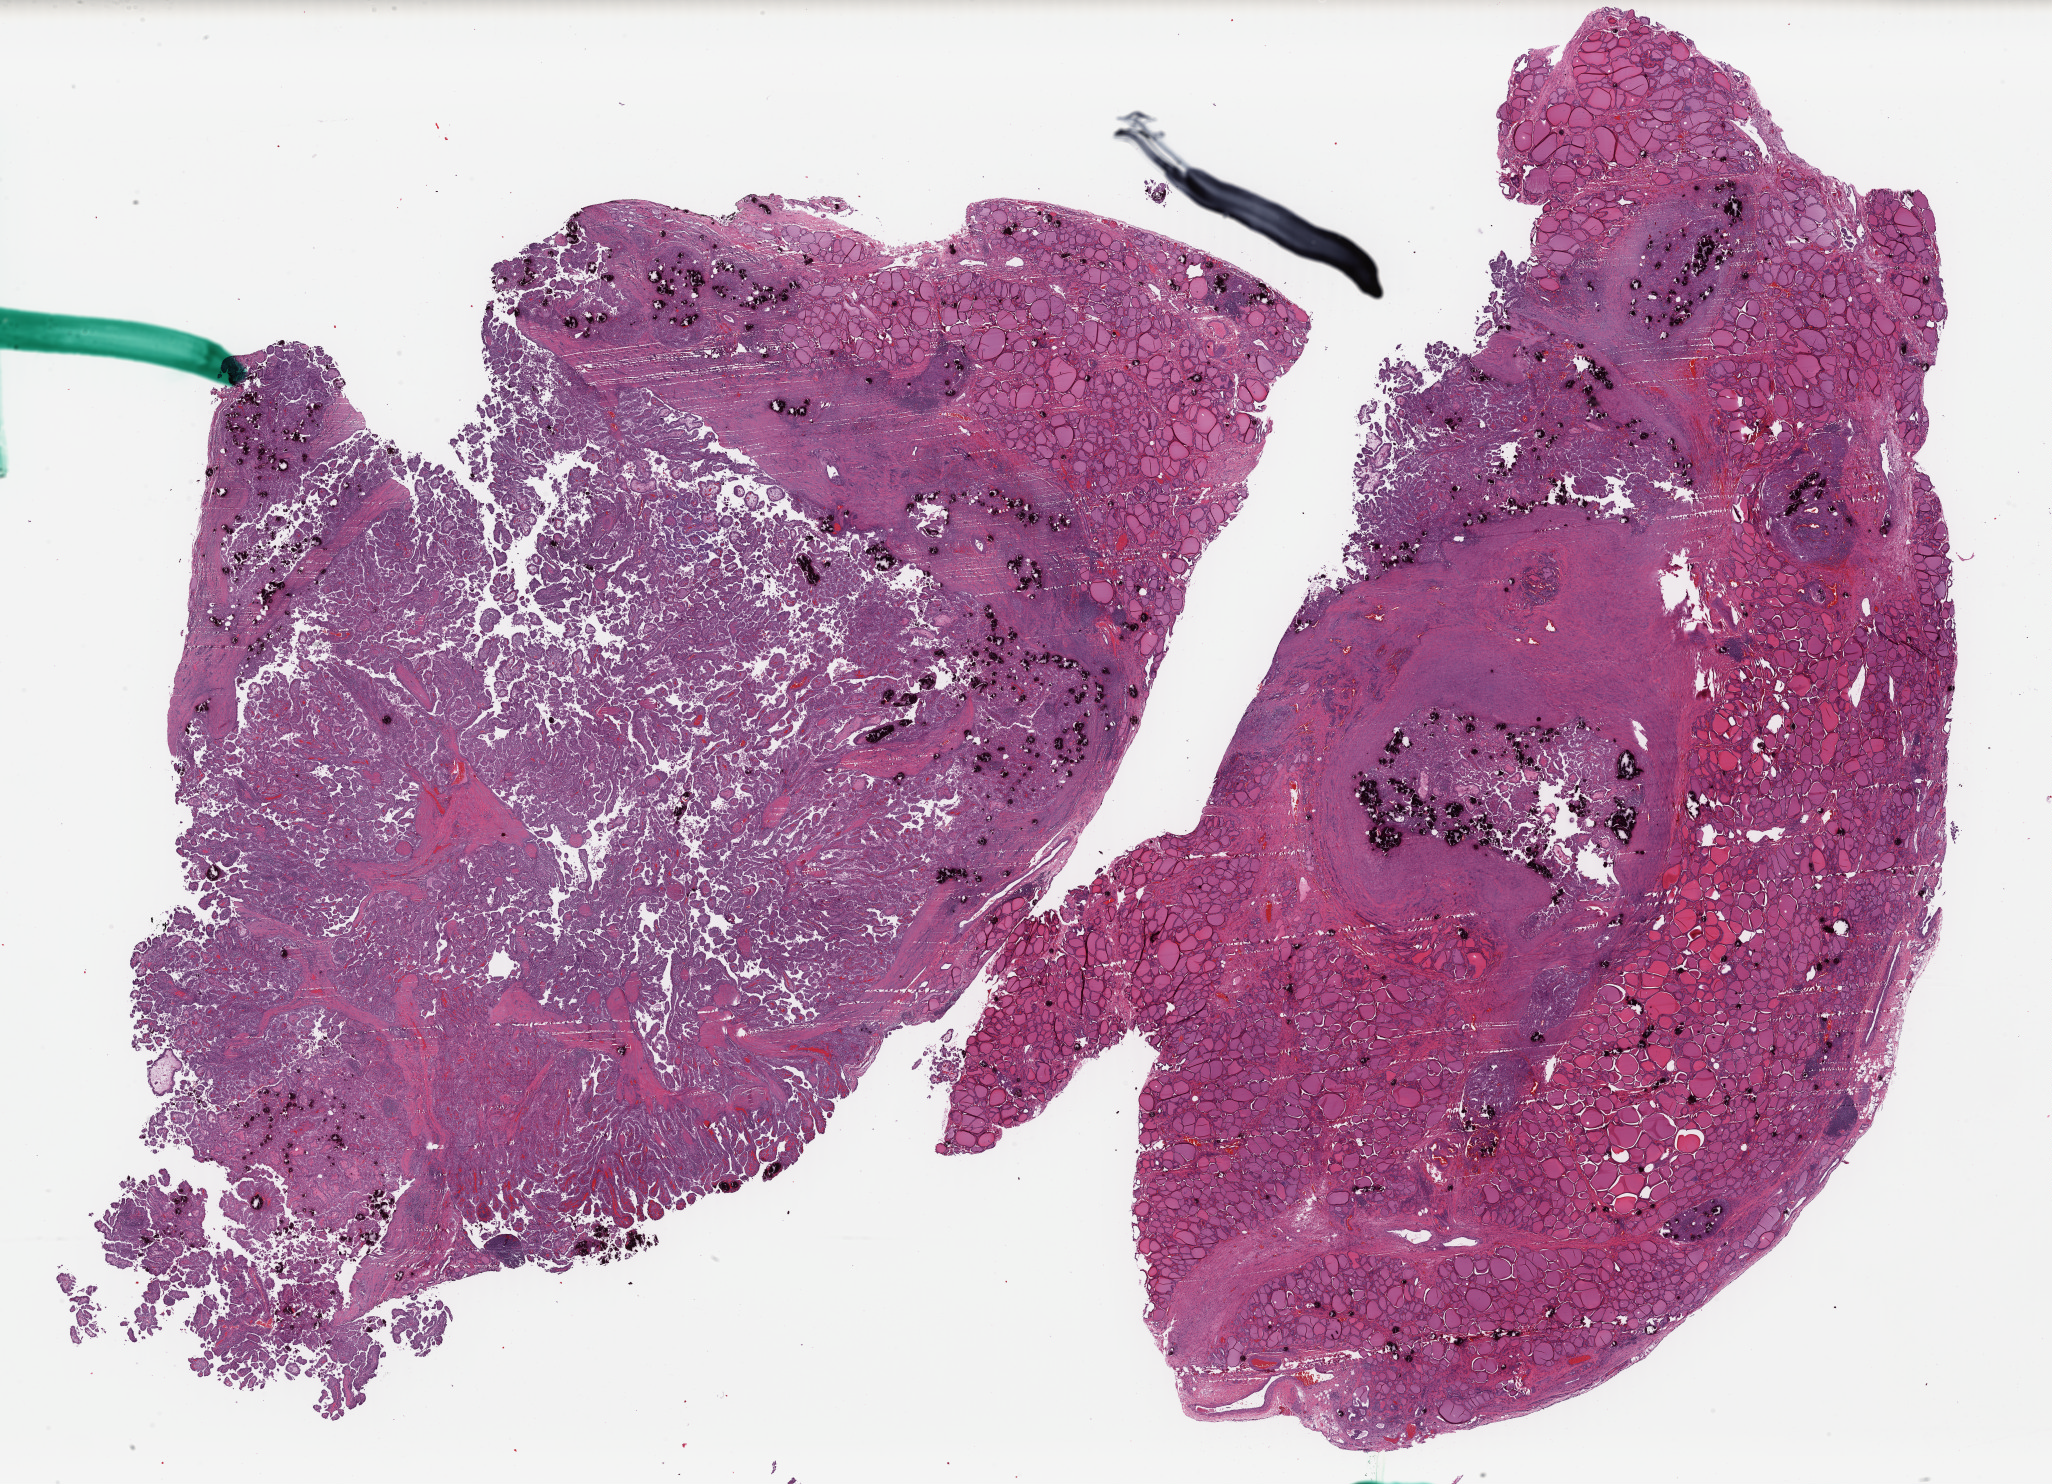
H&E-stained whole-slide image, shown as a low-resolution overview of the whole scanned area (about 32.4 x 23.4 mm, slide scanned at 40x), FFPE section, primary tumour sample from the thyroid. Male, age 22 years at initial diagnosis.
- lymph nodes positive (case pathology): 5 of 5 examined
- AJCC pathologic stage: I (7th edition)
- laterality: bilateral
- histologic diagnosis: Nonencapsulated sclerosing carcinoma (thyroid gland)